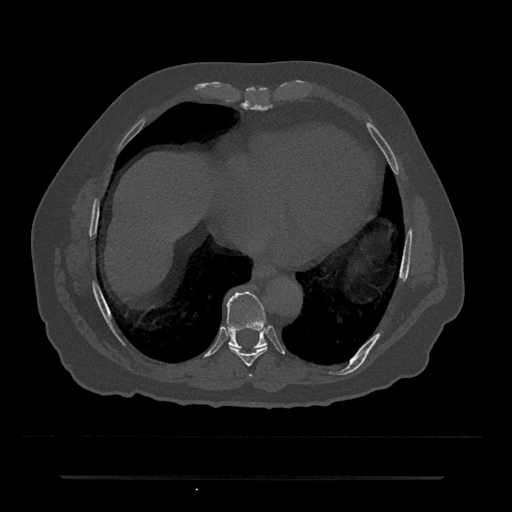
CT including the spine, one axial slice. Slice 308 of 797 in the series (ordered by position). 120 kVp. Bone window (W 1800 / L 400 HU). 512 × 512 image matrix. Patient: male, 69 years. From the clinical record (not read from this slice): primary cancer: prostate.
Structures marked on this image (semi-automatic segmentation, software-assisted and operator-edited):
- T7 vertebra: bounding box [x1, y1, x2, y2] px = [250, 375, 252, 377]
- T8 vertebra: [229, 345, 268, 366]
- T9 vertebra: [227, 291, 267, 349]